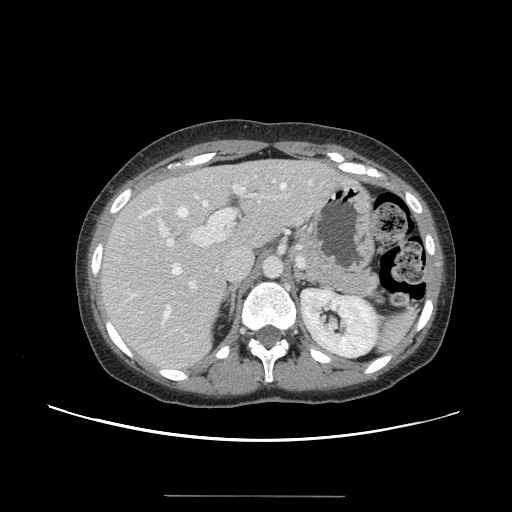
Contrast-enhanced abdominal CT, one axial slice; slice 91 of 144 in the series (ordered by position); 120 kVp; intravenous contrast given; soft-tissue window (W 400 / L 40 HU); 2.5 mm slice thickness; 512 × 512 image matrix, field of view 380 × 380 mm. Female patient, age 53 years. Case-level facts recorded for this patient, not image findings: diagnosis: colorectal cancer liver metastases, imaged before liver resection; multiple liver metastases: yes; largest metastasis: 1.1 cm; chemotherapy before resection: no.
Outlined on this slice (manually delineated by an expert):
- hepatic veins: bounding box [x1, y1, x2, y2] px = [133, 182, 311, 324]
- liver: [100, 160, 343, 371]
- planned liver remnant (the part of the liver to remain after resection): [101, 160, 312, 298]
- portal vein (with intrahepatic branches): [158, 178, 287, 290]